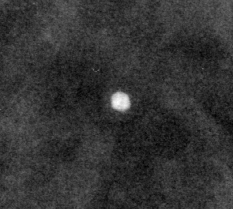
Cropped region of a digitized screen-film mammogram centred on a radiologist-marked abnormality; left breast; CC view.
Marked abnormality: calcifications, morphology lucent center; BI-RADS assessment category 2; subtlety rating 5 on a 1 (subtle) to 5 (obvious) scale; benign; no additional work-up was recommended (benign without callback).